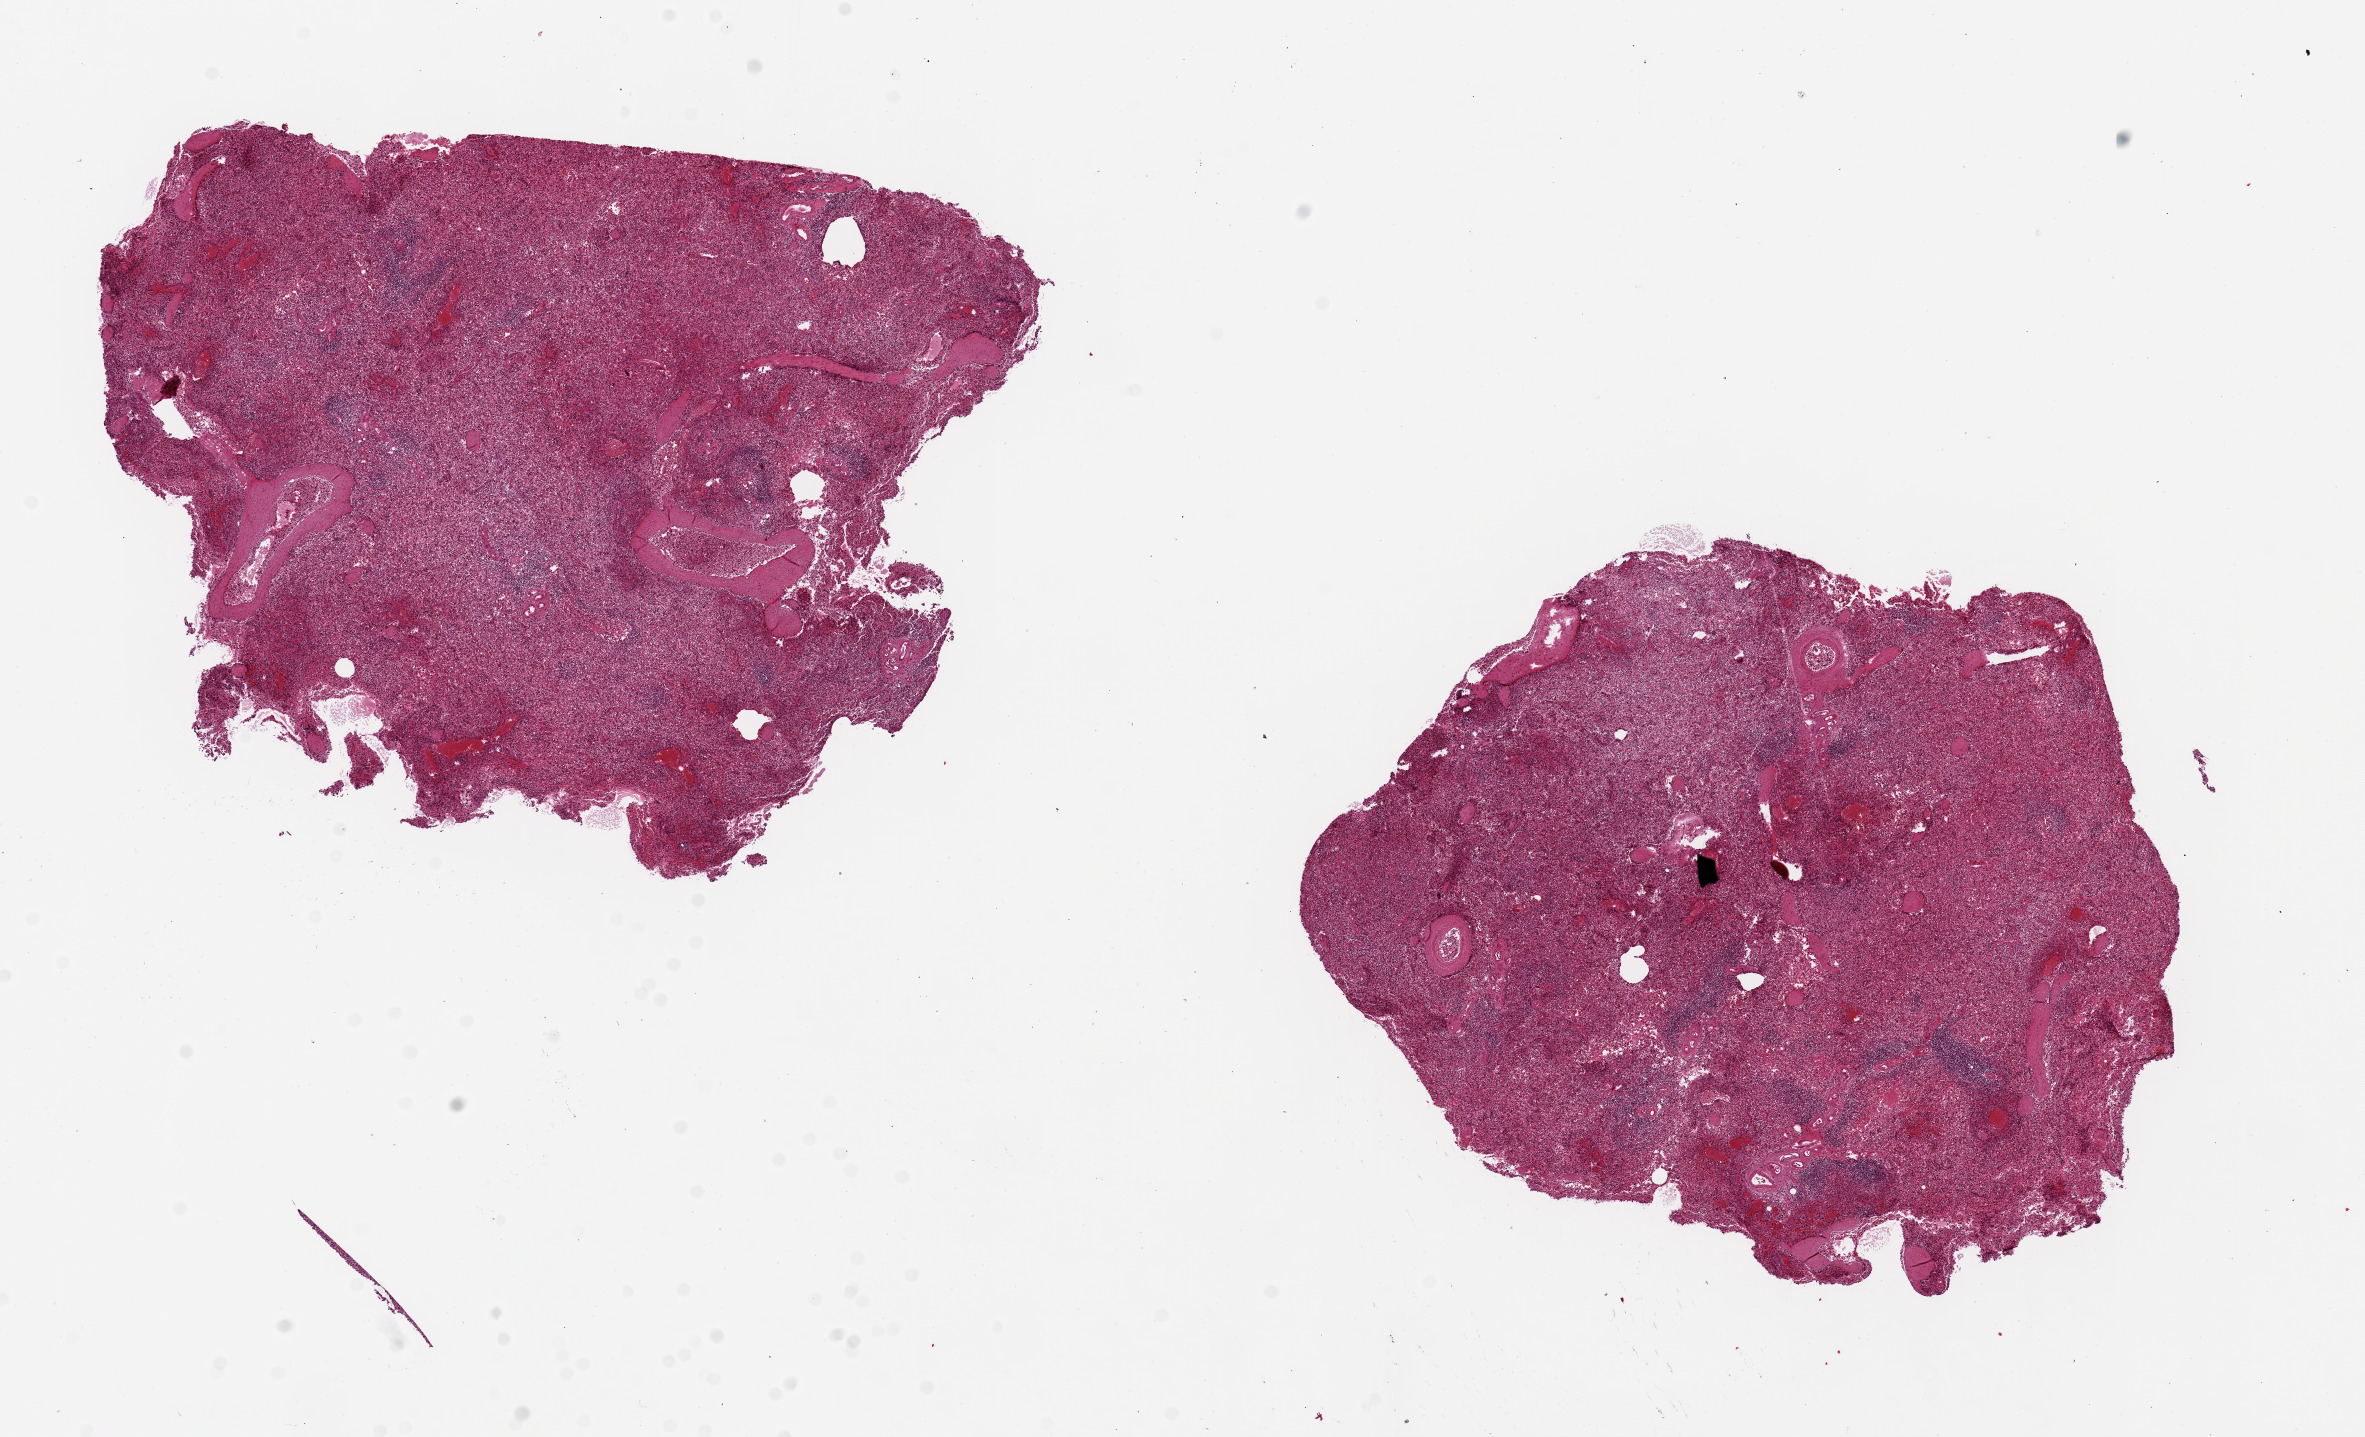
Hematoxylin and eosin (H&E) whole-slide image — a low-resolution overview of the entire scanned area, about 18.7 x 11.4 mm (acquisition: 20x scan). PAXgene-fixed paraffin-embedded (PFPE) section. Target tissue: spleen. Tissue donor sample. Male donor.
Review note (as recorded): 2 pieces, 7x6 & 7x6mm.